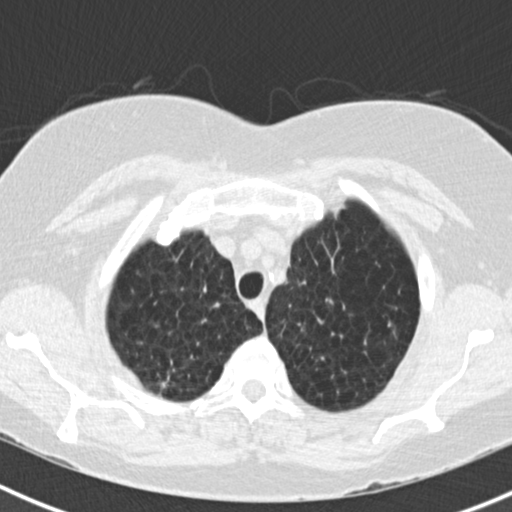
Low-dose screening chest CT, one axial slice; position 147 of 180 along the scan axis; 120 kVp; lung window (W 1500 / L -600 HU); 2 mm slice thickness; 512 × 512 image matrix, field of view 310 × 310 mm.
Outlined on this slice (manually delineated by an expert):
- lesion 1 (tumor, upper lobe of right lung): bounding box [x1, y1, x2, y2] px = [161, 377, 169, 388]